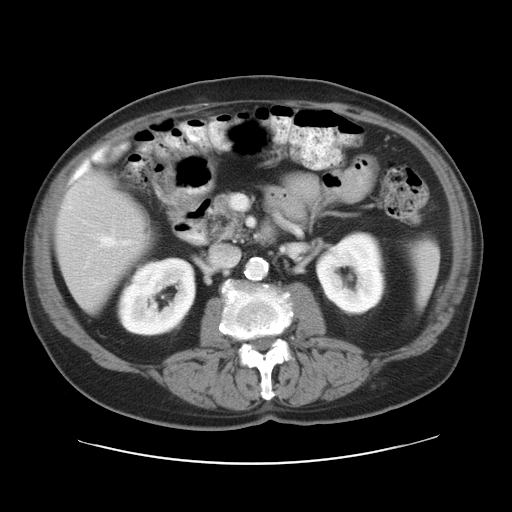
Contrast-enhanced abdominal CT, one axial slice; position 12 of 28 along the scan axis; 120 kVp; soft-tissue window (W 400 / L 40 HU); 7.5 mm slice thickness; 512 × 512 image matrix. Male patient, age 74 years. Case-level facts recorded for this patient, not image findings: diagnosis: colorectal cancer liver metastases, imaged before liver resection; multiple liver metastases: no; largest metastasis: 5 cm; disease in both lobes: no.
Structures marked on this image (outlined manually by an expert reader):
- hepatic veins: bounding box (x1, y1, x2, y2) in pixels: (100, 235, 132, 247)
- liver: (57, 177, 148, 309)
- planned liver remnant (the part of the liver to remain after resection): (57, 176, 148, 309)